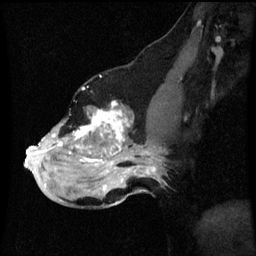
Breast MRI (dynamic contrast-enhanced), one sagittal slice; position 34 of 60 along the scan axis; dynamic contrast-enhanced series, image 2 of 3 at this slice position (ordered by acquisition); 1.5 T; TE 4.2 ms, TR 8.9 ms; 2 mm slice thickness; 256 × 256 image matrix, field of view 200 × 200 mm. Patient: female, 49 years. From the clinical record (not read from this slice): setting: breast cancer imaged before/during neoadjuvant chemotherapy; receptor status: HR-positive, HER2-negative.
Structures marked on this image (semi-automatically segmented with operator editing):
- analysis volume of interest (the breast-tissue region the enhancement analysis was run in; not a lesion): bounding box [x1, y1, x2, y2] px = [26, 102, 159, 199]
- tumour enhancement mask (voxels above the 70 % enhancement threshold inside the analysis volume of interest): [26, 104, 157, 187]